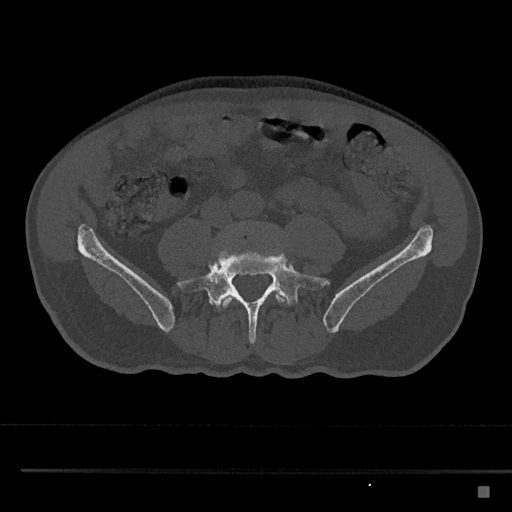
CT including the spine, one axial slice. Position 596 of 797 along the scan axis. Reconstruction kernel Br40s/3. 120 kVp. Bone window (W 1800 / L 400 HU). 0.5 mm slice thickness. 512 × 512 image matrix. Patient: male, 59 years. Case-level facts recorded for this patient, not image findings: primary cancer: prostate.
Outlined on this slice (semi-automatic segmentation, software-assisted and operator-edited):
- L4 vertebra: box from (x=216, y=225) to (x=289, y=310) px
- L5 vertebra: (x=176, y=240)–(x=331, y=344)